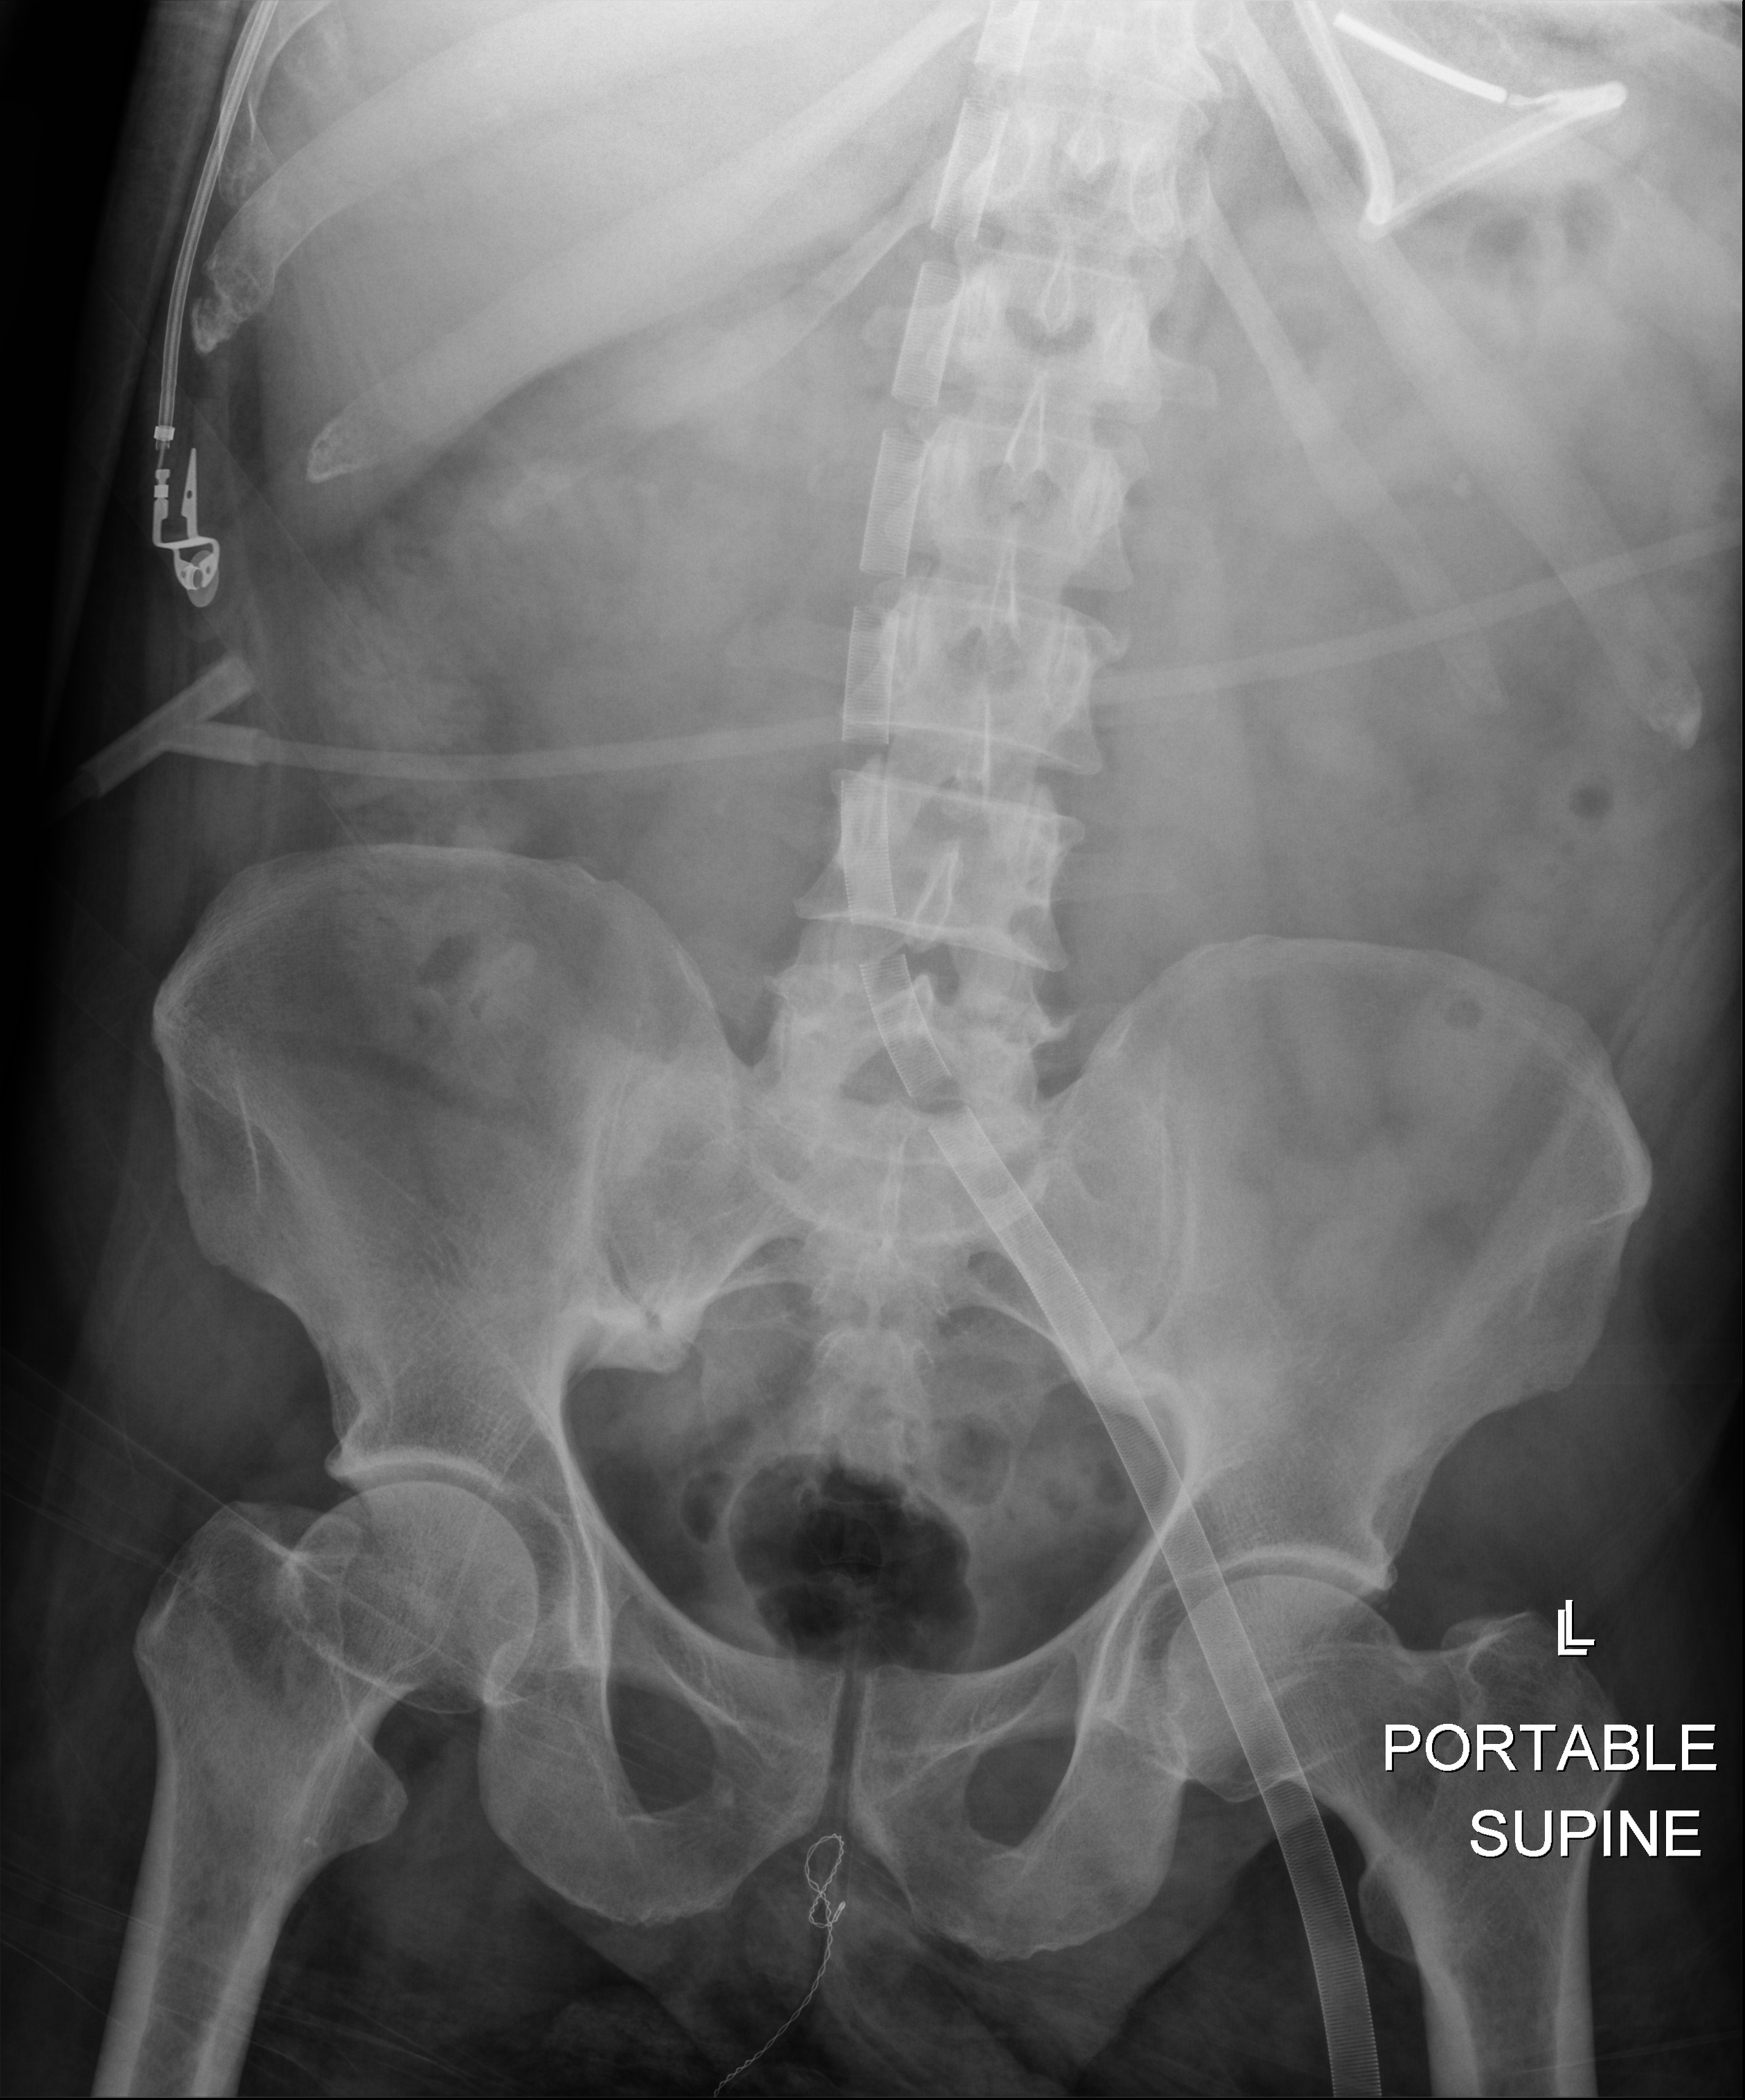
Portable abdomen radiograph. Male patient hospitalised with COVID-19, age 18–59 years.
From the hospital-stay record, not from the radiograph (when in the stay this image was taken is not recorded):
- mechanically ventilated during this hospital stay: yes